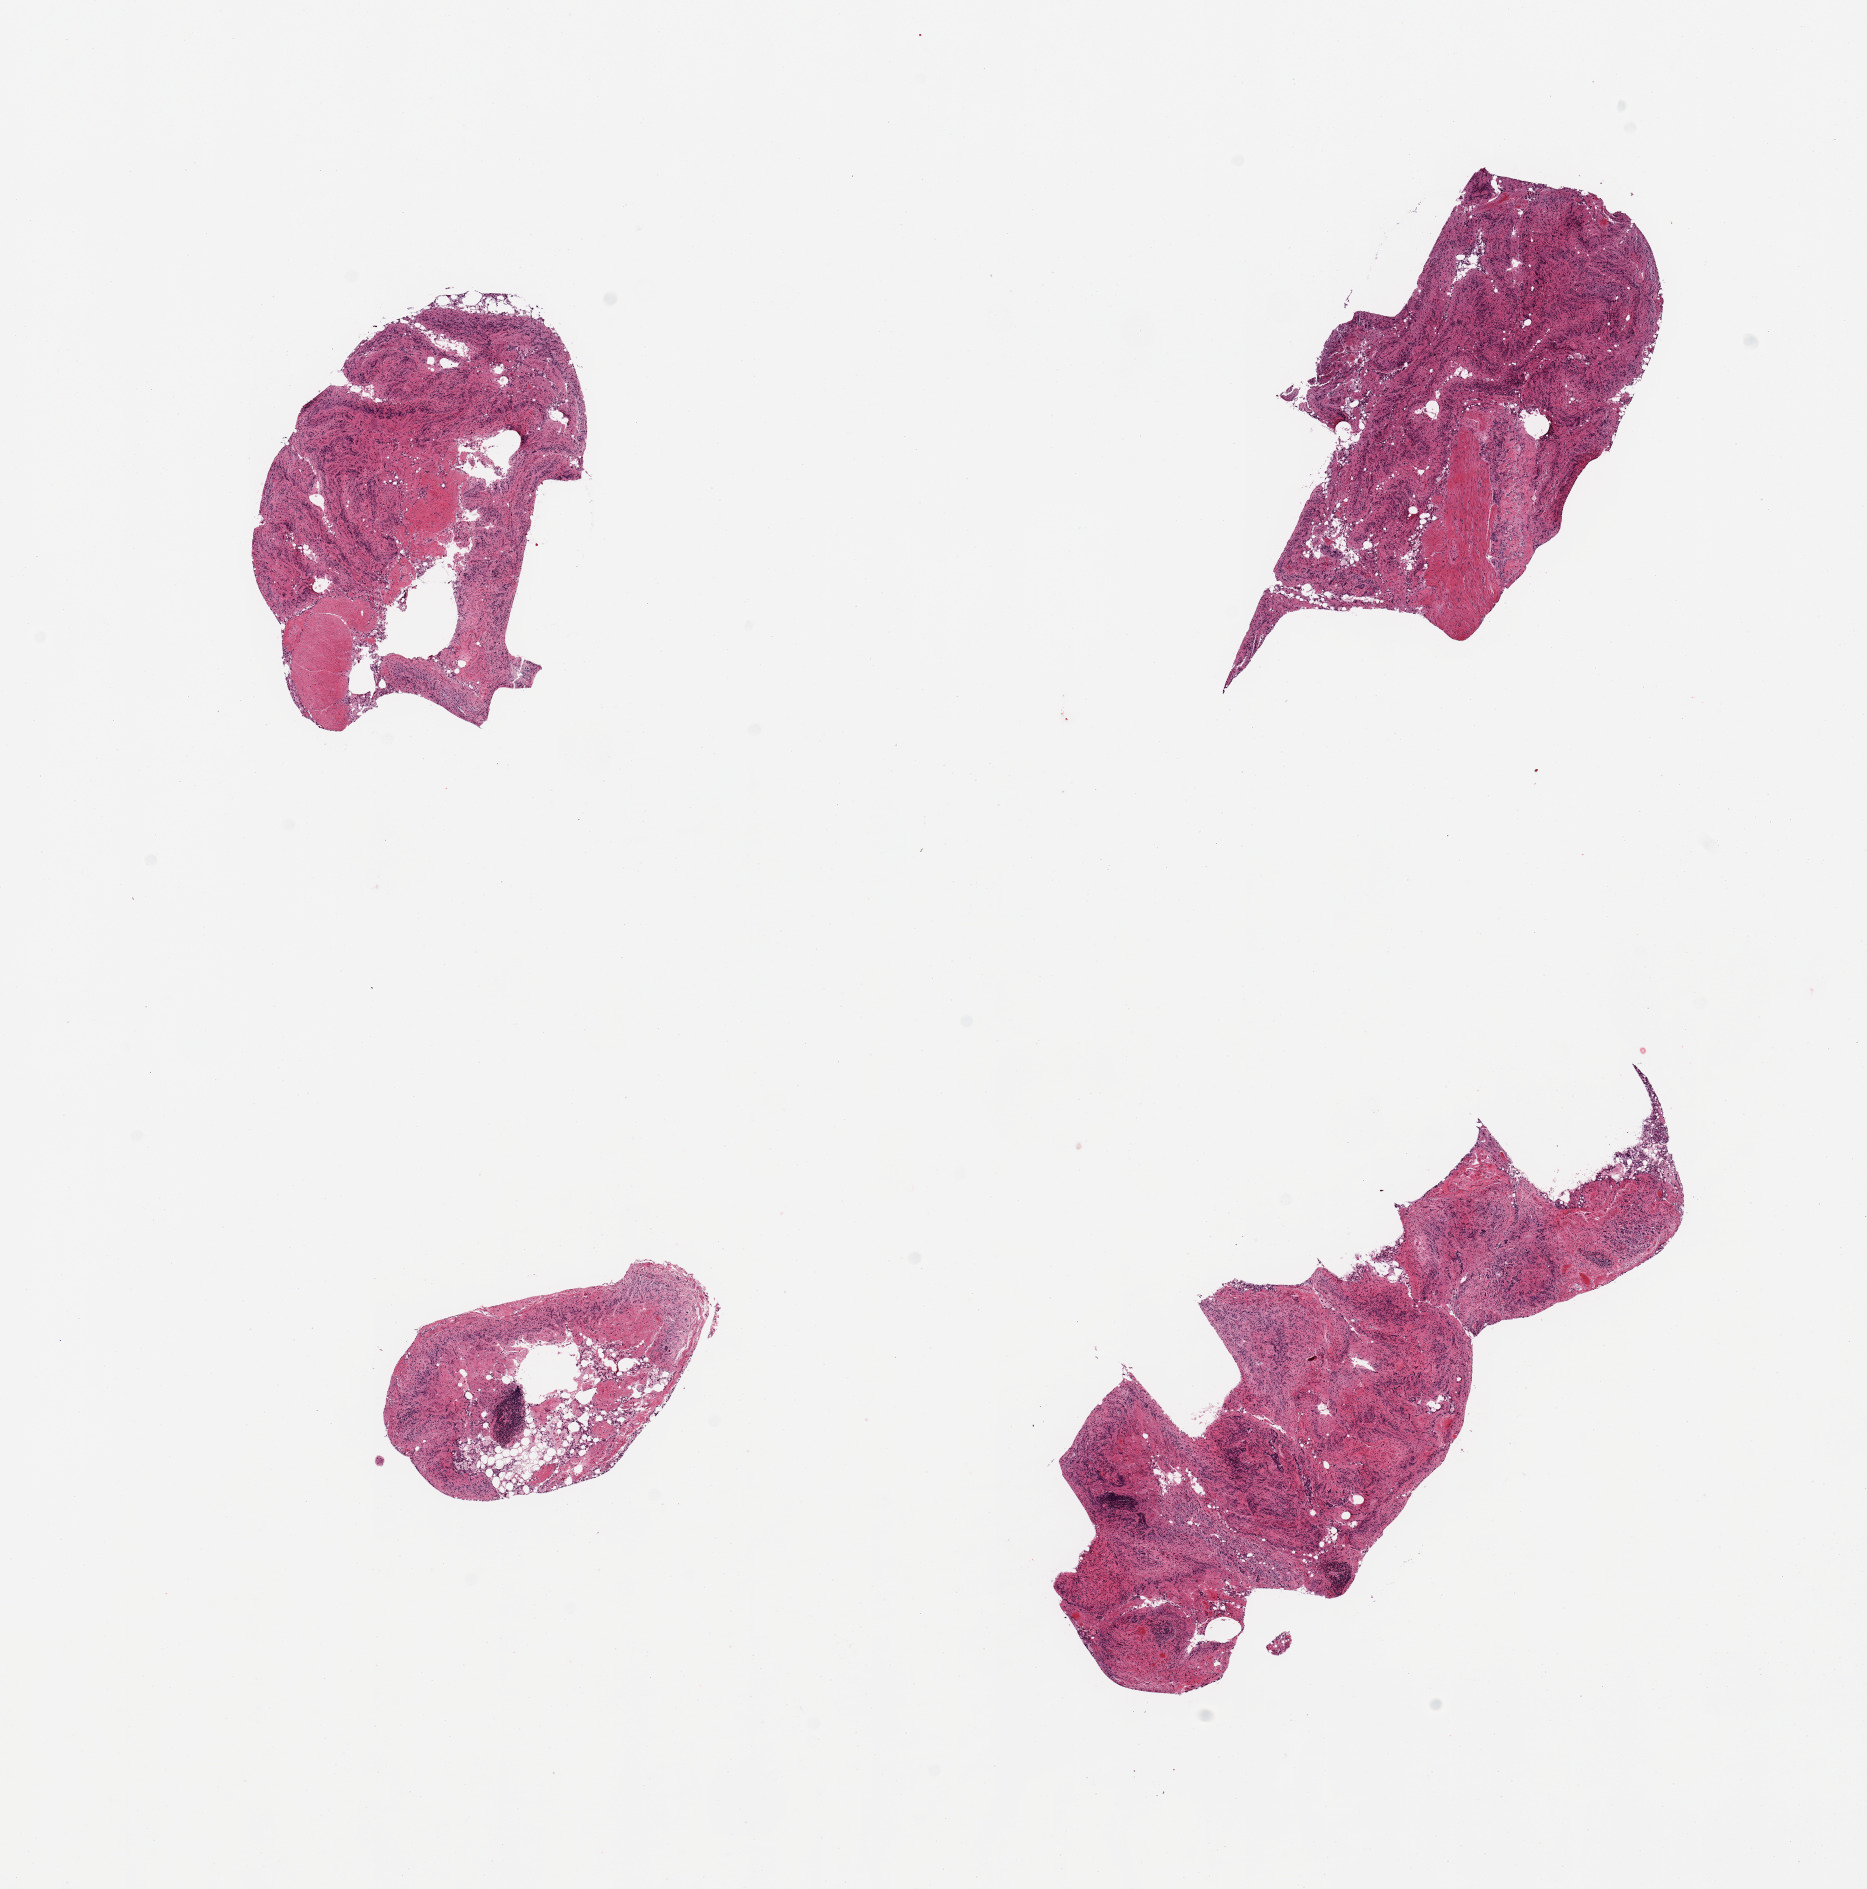
Digitized hematoxylin and eosin (H&E)-stained section — shown as a low-resolution overview of the whole scanned area (about 14.8 x 14.9 mm), PAXgene-fixed, paraffin-embedded tissue, sampled site (target tissue): ileum, tissue donor sample. Donor sex: male.
* review note (as recorded): 4 pieces; predominantly autolyzed mucosa with some muscularis, no significant/residual lymphoid tissue